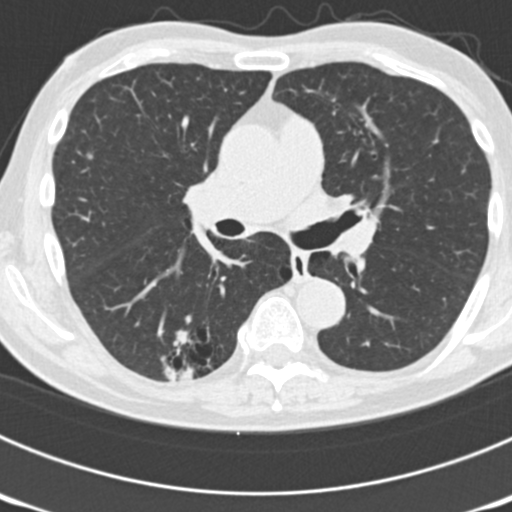
Low-dose screening chest CT, one axial slice; slice 107 of 177 in the series (ordered by position); 120 kVp; lung window (W 1500 / L -600 HU); 512 × 512 image matrix, field of view 300 × 300 mm.
Outlined on this slice (outlined manually by an expert reader):
- lesion 2 (nodule, upper lobe of right lung): bounding box <86,153,94,160> (left, top, right, bottom; pixels)
- lesion 5 (nodule, lower lobe of right lung): <163,361,196,383>
- lesion 7 (nodule, lower lobe of right lung): <169,328,189,347>